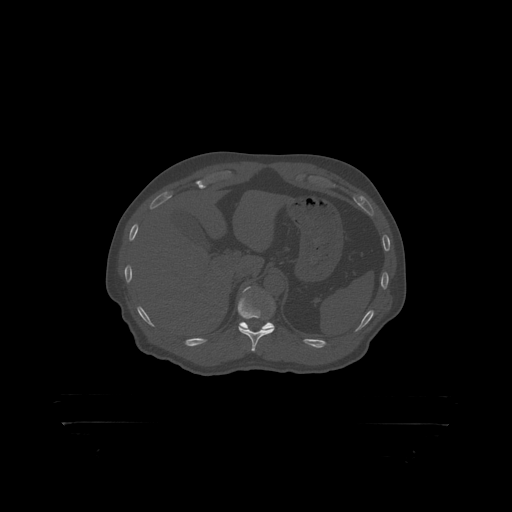
CT including the spine, one axial slice. Slice 370 of 399 in the series (ordered by position). Reconstruction kernel STANDARD. Bone window (W 1800 / L 400 HU). 1.25 mm slice thickness. 512 × 512 image matrix, field of view 650 × 650 mm. Patient: male, 46 years. From the clinical record (not read from this slice): primary cancer: skin.
Outlined on this slice (semi-automatic segmentation, software-assisted and operator-edited):
- T11 vertebra: bounding box <238,292,275,319> (left, top, right, bottom; pixels)
- T12 vertebra: <244,287,251,292>